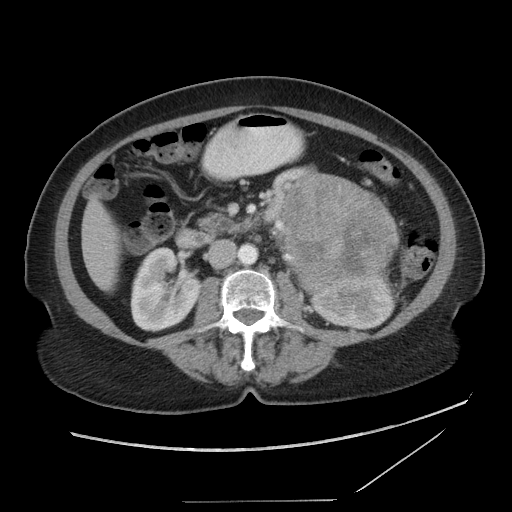
Contrast-enhanced abdominal CT, one axial slice. Position 46 of 86 along the scan axis. Reconstruction kernel STANDARD. 120 kVp. Soft-tissue window (W 400 / L 40 HU). 5 mm slice thickness. 512 × 512 image matrix, field of view 398 × 398 mm. Female patient, age 77 years. From the clinical record (not read from this slice): diagnosis: adrenocortical carcinoma; tumour side: left adrenal; tumour size at pathology: 13.1 cm; Ki-67 index: 10 %; stage (as recorded): 3.
Annotated regions visible in this slice (semi-automatic segmentation, software-assisted and operator-edited):
- mass: bounding box <285,177,397,294> (left, top, right, bottom; pixels)